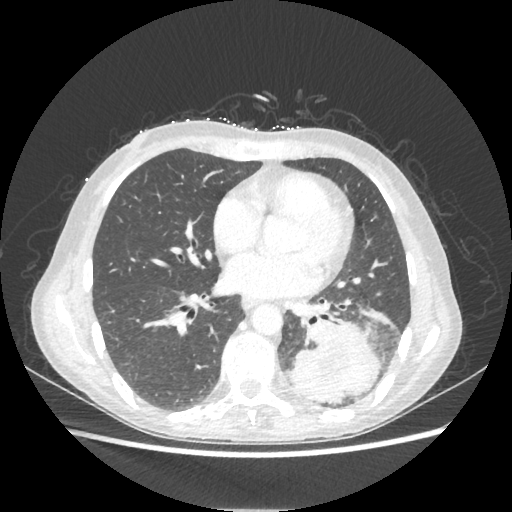
Chest CT, one axial slice; position 99 of 221 along the scan axis; reconstruction kernel STANDARD; lung window (W 1500 / L -600 HU); 1.25 mm slice thickness; 512 × 512 image matrix. Female patient, age 53 years. Case-level facts recorded for this patient, not image findings: clinical TNM (as recorded): T3 N0 M0.
Outlined on this slice (rectangle marked by the reading radiologist):
- lung tumour (recorded histology: adenocarcinoma): bounding box (x1, y1, x2, y2) in pixels: (284, 321, 380, 404)